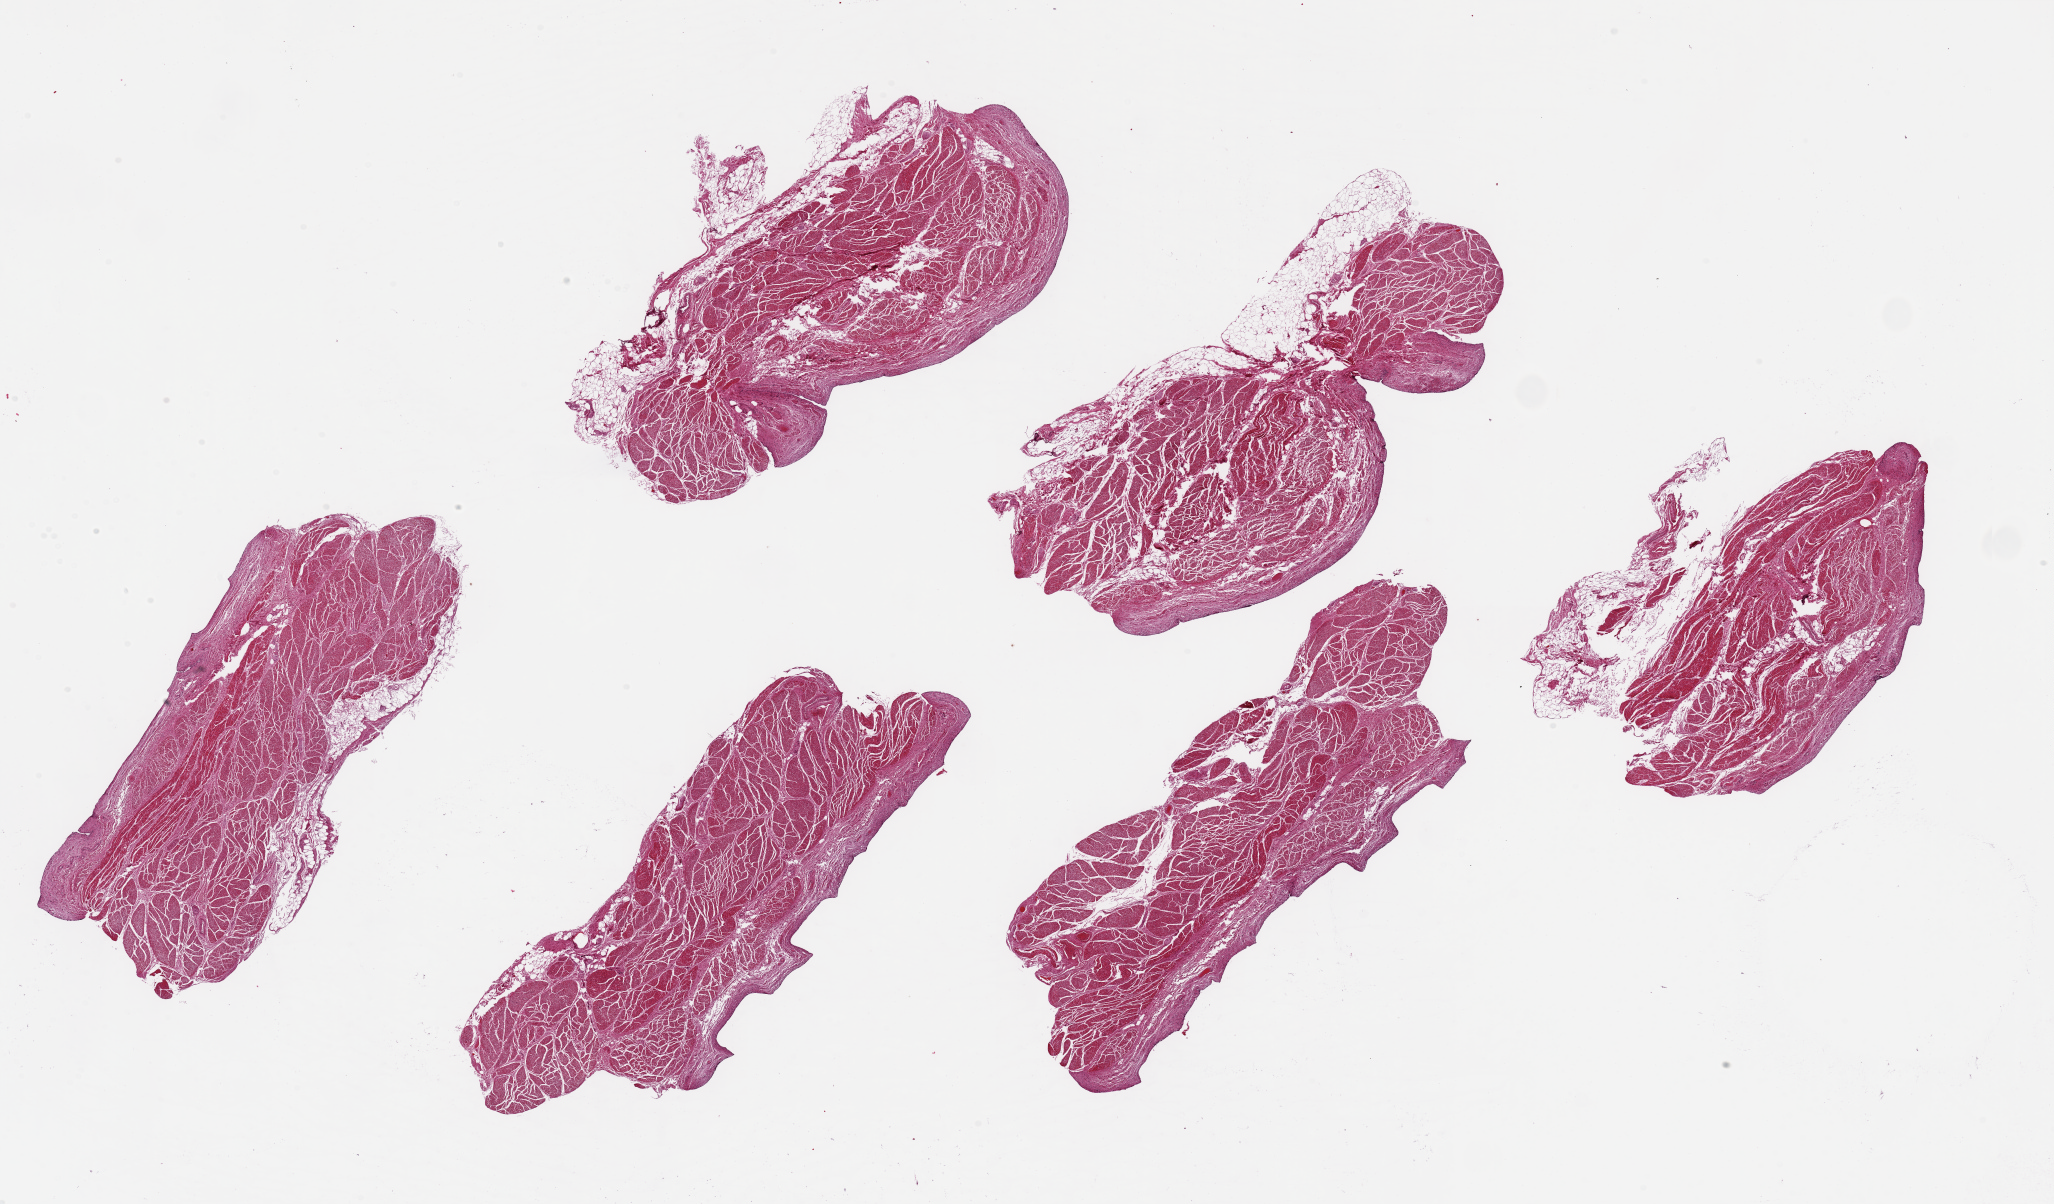
Whole-slide image, haematoxylin and eosin stain, low-resolution overview of the scanned area, about 32.5 x 19.0 mm (acquisition: 20x scan), PAXgene-fixed paraffin-embedded (PFPE) section, section of urinary bladder (target tissue), tissue donor sample. Donor: male.
* pathologist's review note for this sample: 6 pieces, ~10x2.5mm. Urothelium completely sloughed